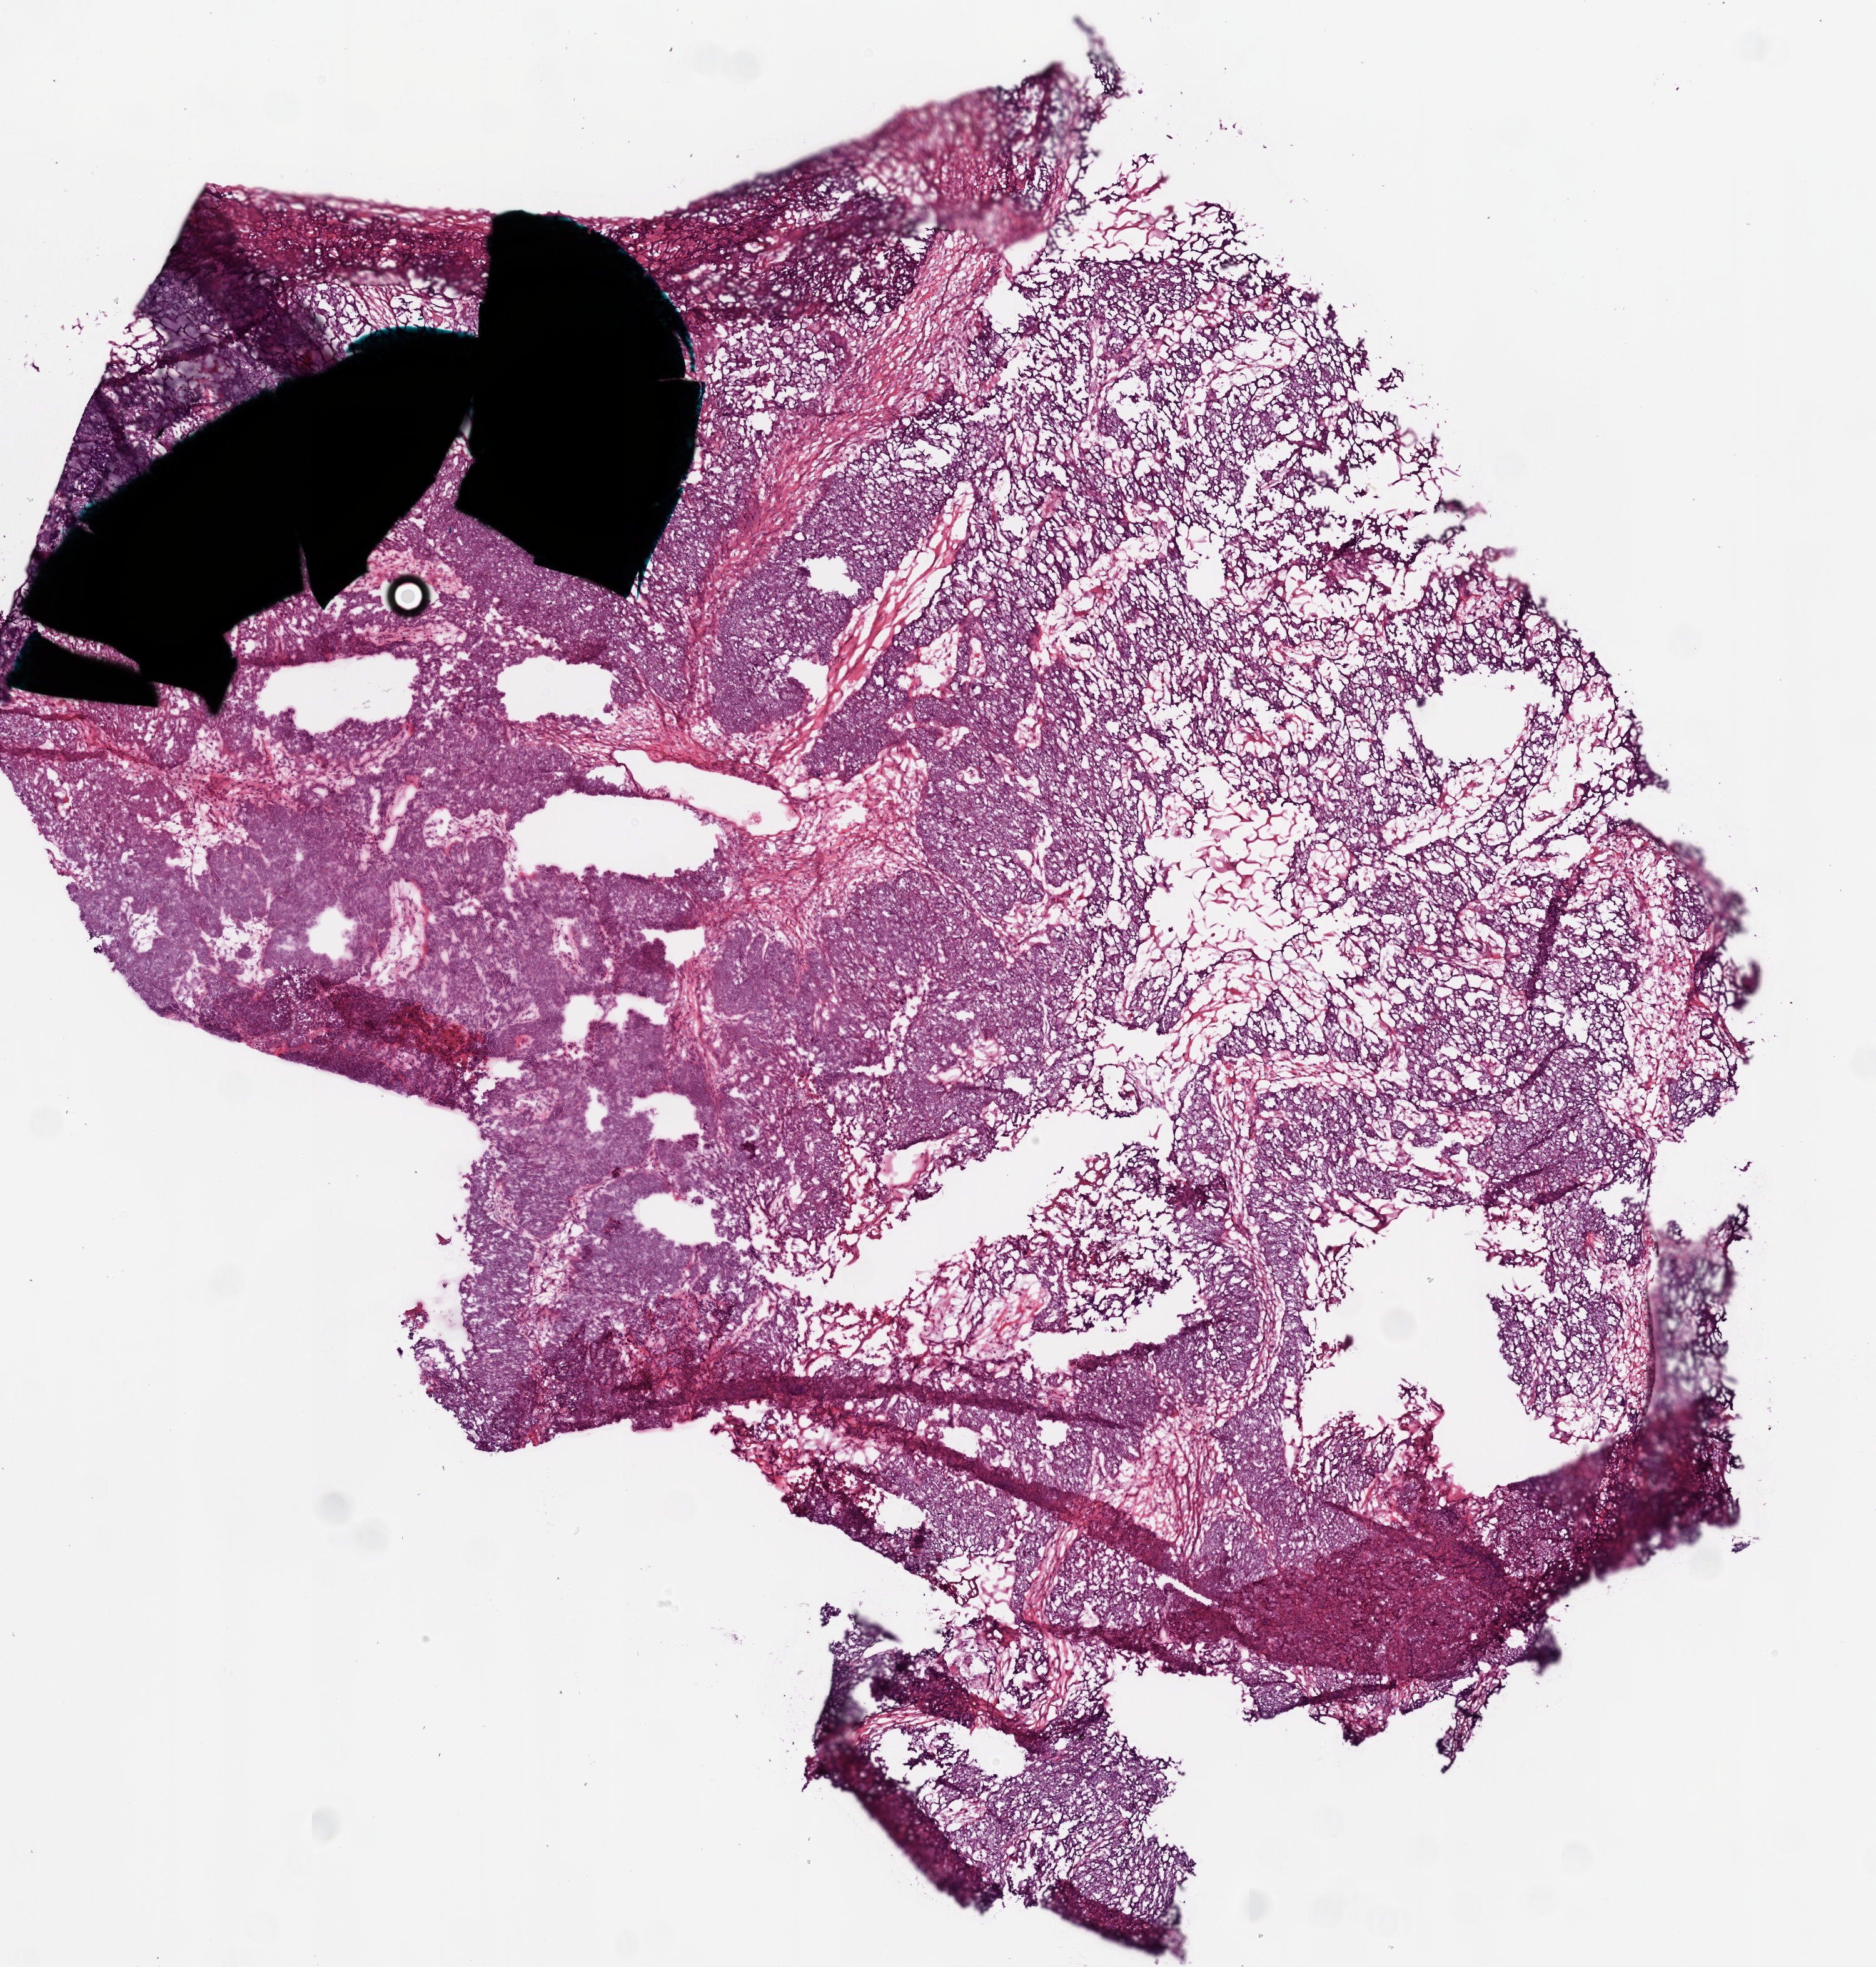
Digitized Hematoxylin and eosin (H&E) stained tissue section (whole slide), shown as a low-resolution overview of the whole scanned area (about 6.0 x 6.3 mm); frozen section; primary tumour sample from the ovary. Female patient; age at initial diagnosis 43 years. Histologic grade: G3 (poorly differentiated). Slide review estimates, as recorded: tumour cells 90%, tumour nuclei 90%, normal cells 0%, stromal cells 10%, necrosis 0%.
- FIGO stage: IIIC
- diagnosis: Serous cystadenocarcinoma, NOS
- laterality: bilateral